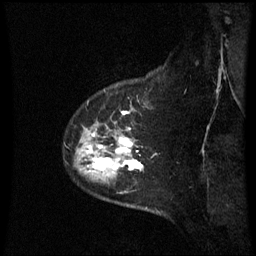
Breast MRI (dynamic contrast-enhanced), one sagittal slice; slice 52 of 60 in the series (ordered by position); dynamic contrast-enhanced series, image 2 of 3 at this slice position (ordered by acquisition); 1.5 T; TE 4.2 ms, TR 8.9 ms; 2.3 mm slice thickness; 256 × 256 image matrix, field of view 210 × 210 mm. Female patient, age 43 years. Case-level facts recorded for this patient, not image findings: setting: breast cancer imaged before/during neoadjuvant chemotherapy; receptor status: HER2-positive.
Annotated regions visible in this slice (semi-automatic segmentation, software-assisted and operator-edited):
- analysis volume of interest (the breast-tissue region the enhancement analysis was run in; not a lesion): bounding box (x1, y1, x2, y2) in pixels: (74, 84, 158, 195)
- tumour enhancement mask (voxels above the 70 % enhancement threshold inside the analysis volume of interest): (88, 112, 144, 172)